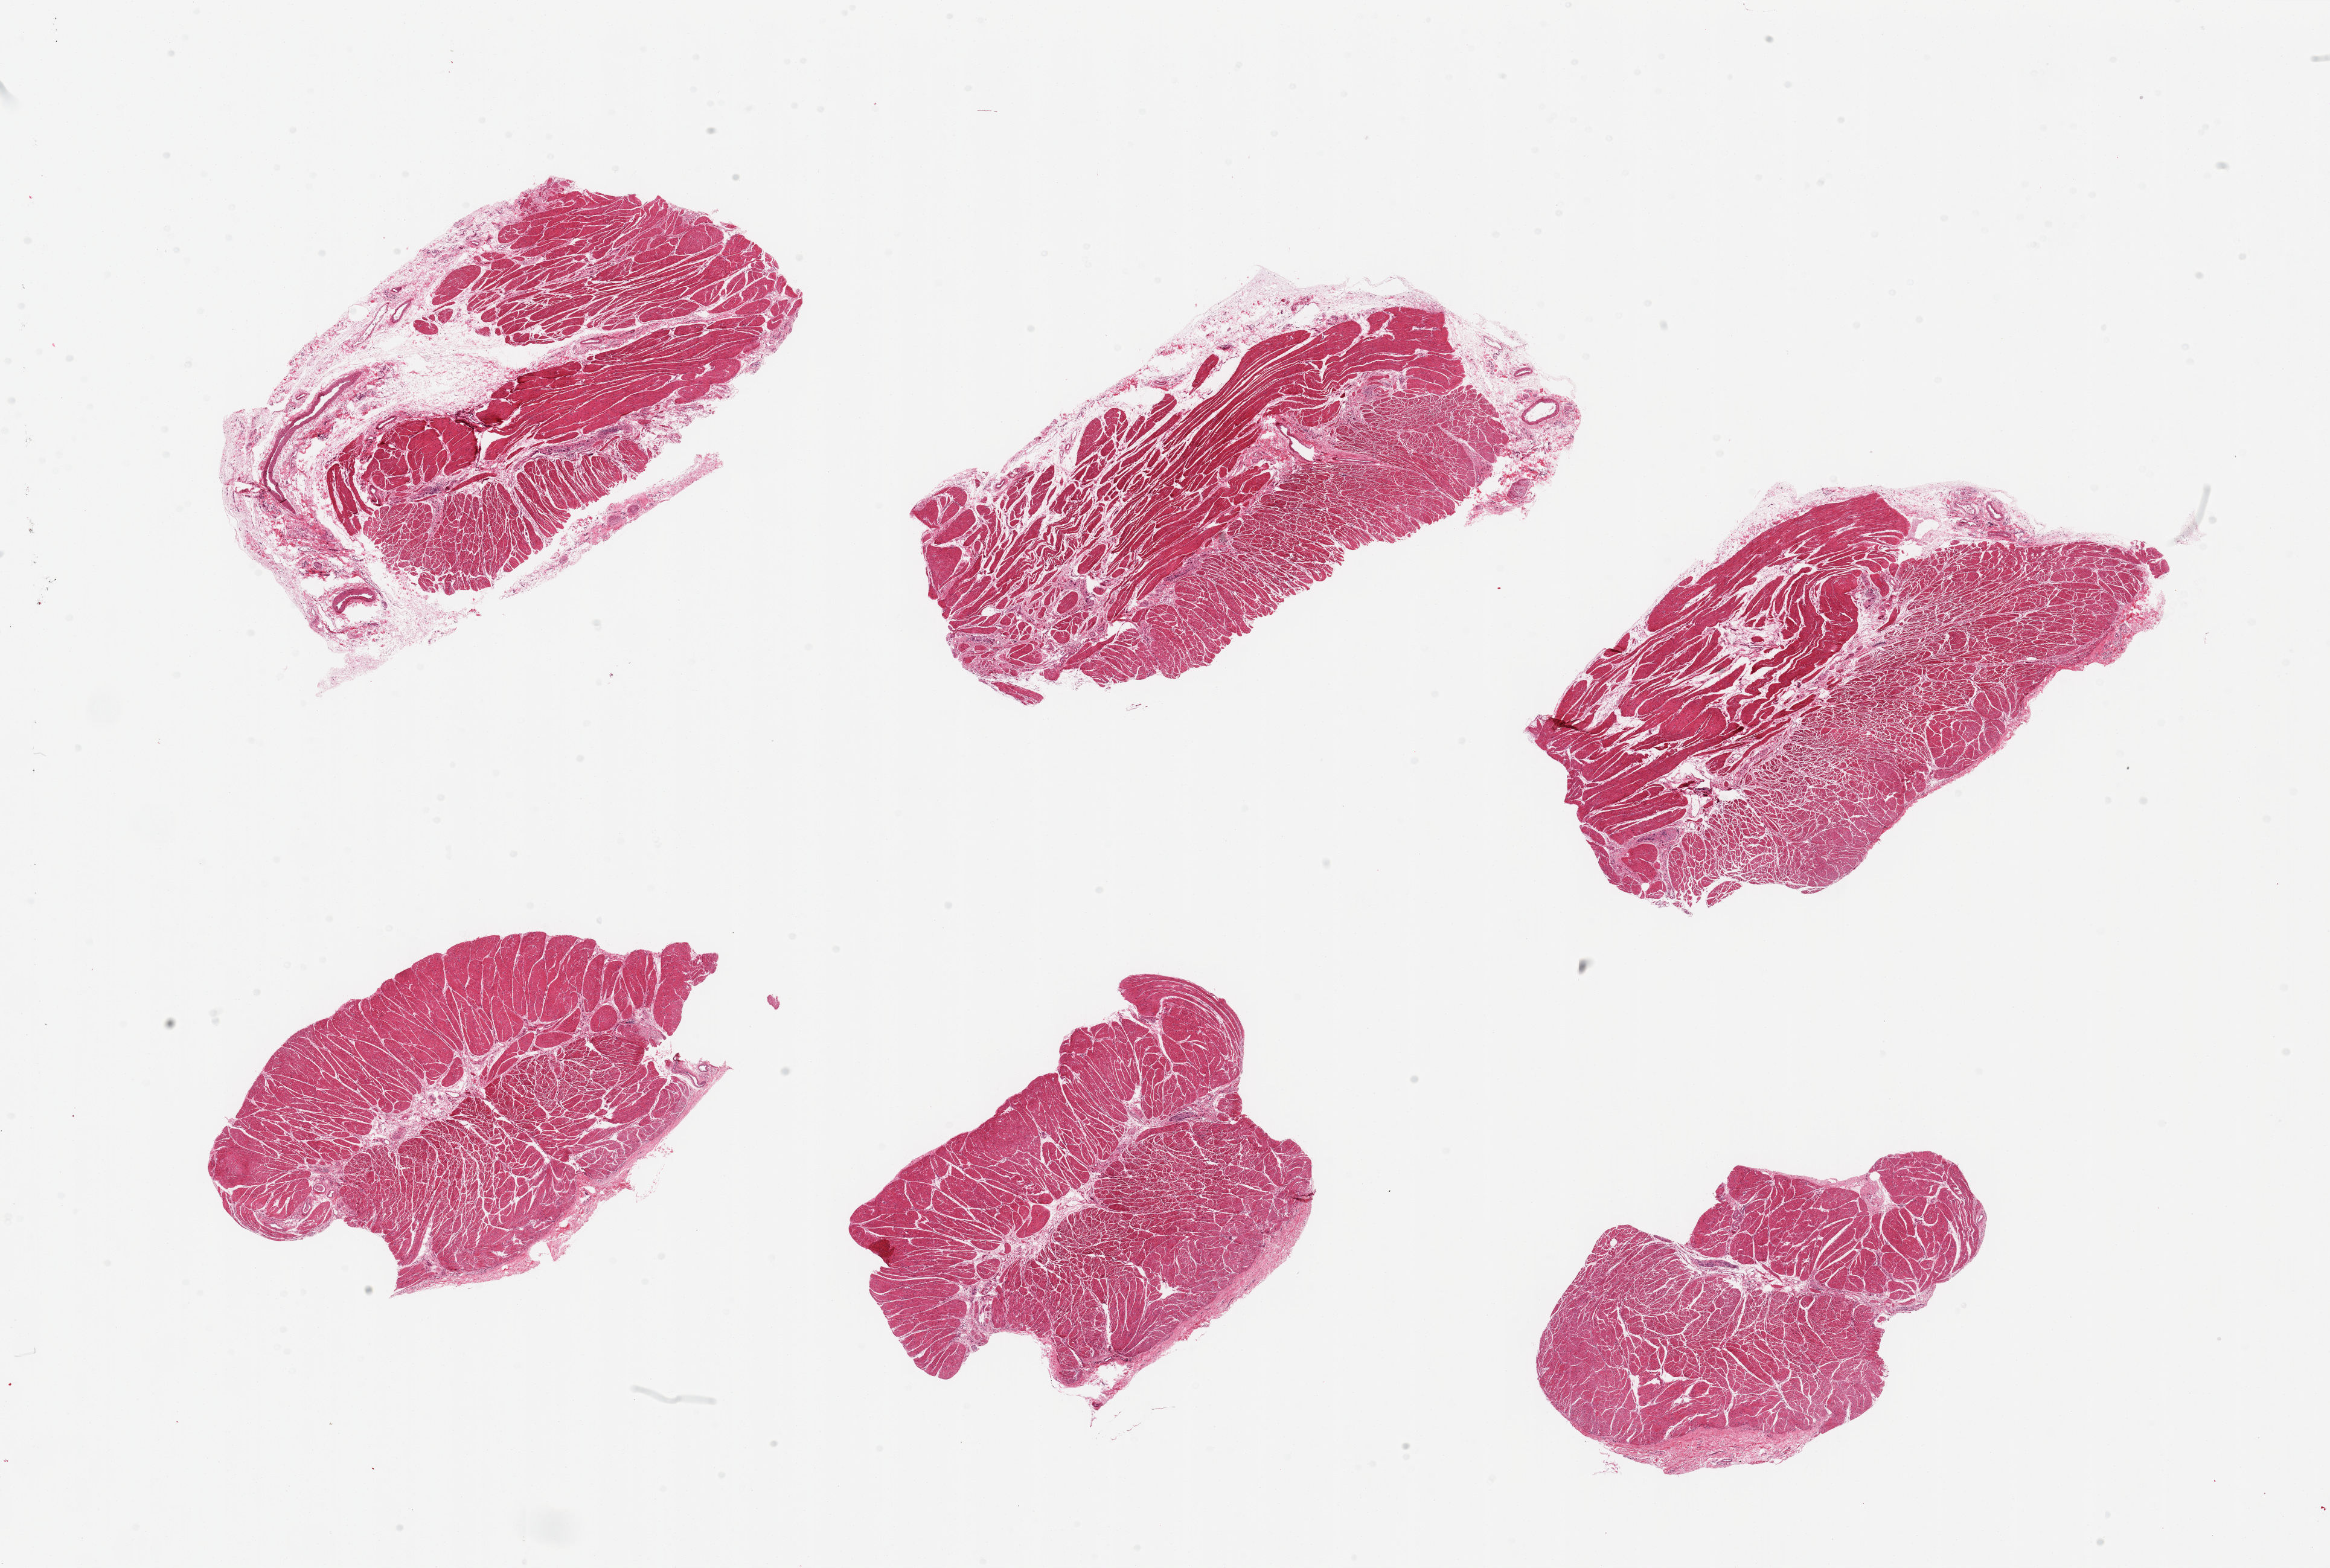
Digitized haematoxylin and eosin-stained section, whole scanned area (about 30.5 x 20.5 mm) shown as a low-resolution overview; PAXgene-fixed paraffin-embedded (PFPE) section; section of esophageal muscle (target tissue); donor tissue sample.
- reviewer comment on this tissue sample: 6 pieces, confirmed target muscularis